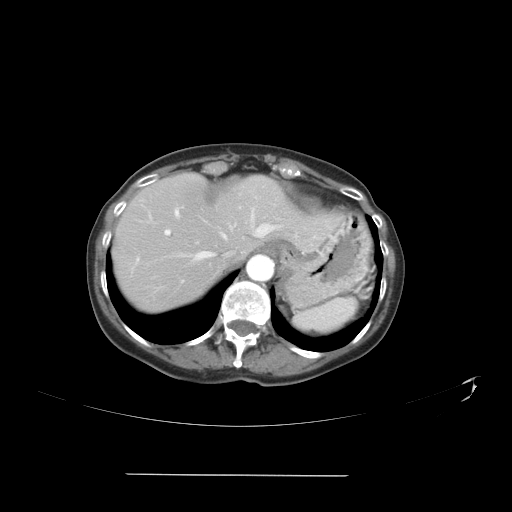
Contrast-enhanced abdominal CT, one axial slice; position 31 of 41 along the scan axis; soft-tissue window (W 400 / L 40 HU); 5 mm slice thickness; 512 × 512 image matrix. Female patient, age 74 years. Case-level facts recorded for this patient, not image findings: diagnosis: colorectal cancer liver metastases, imaged before liver resection; multiple liver metastases: yes; largest metastasis: 3.3 cm; disease in both lobes: yes.
Structures marked on this image (expert manual segmentation):
- hepatic veins: bounding box [x1, y1, x2, y2] px = [176, 205, 276, 263]
- liver: [115, 174, 337, 310]
- planned liver remnant (the part of the liver to remain after resection): [118, 174, 332, 258]
- portal vein (with intrahepatic branches): [165, 210, 183, 282]